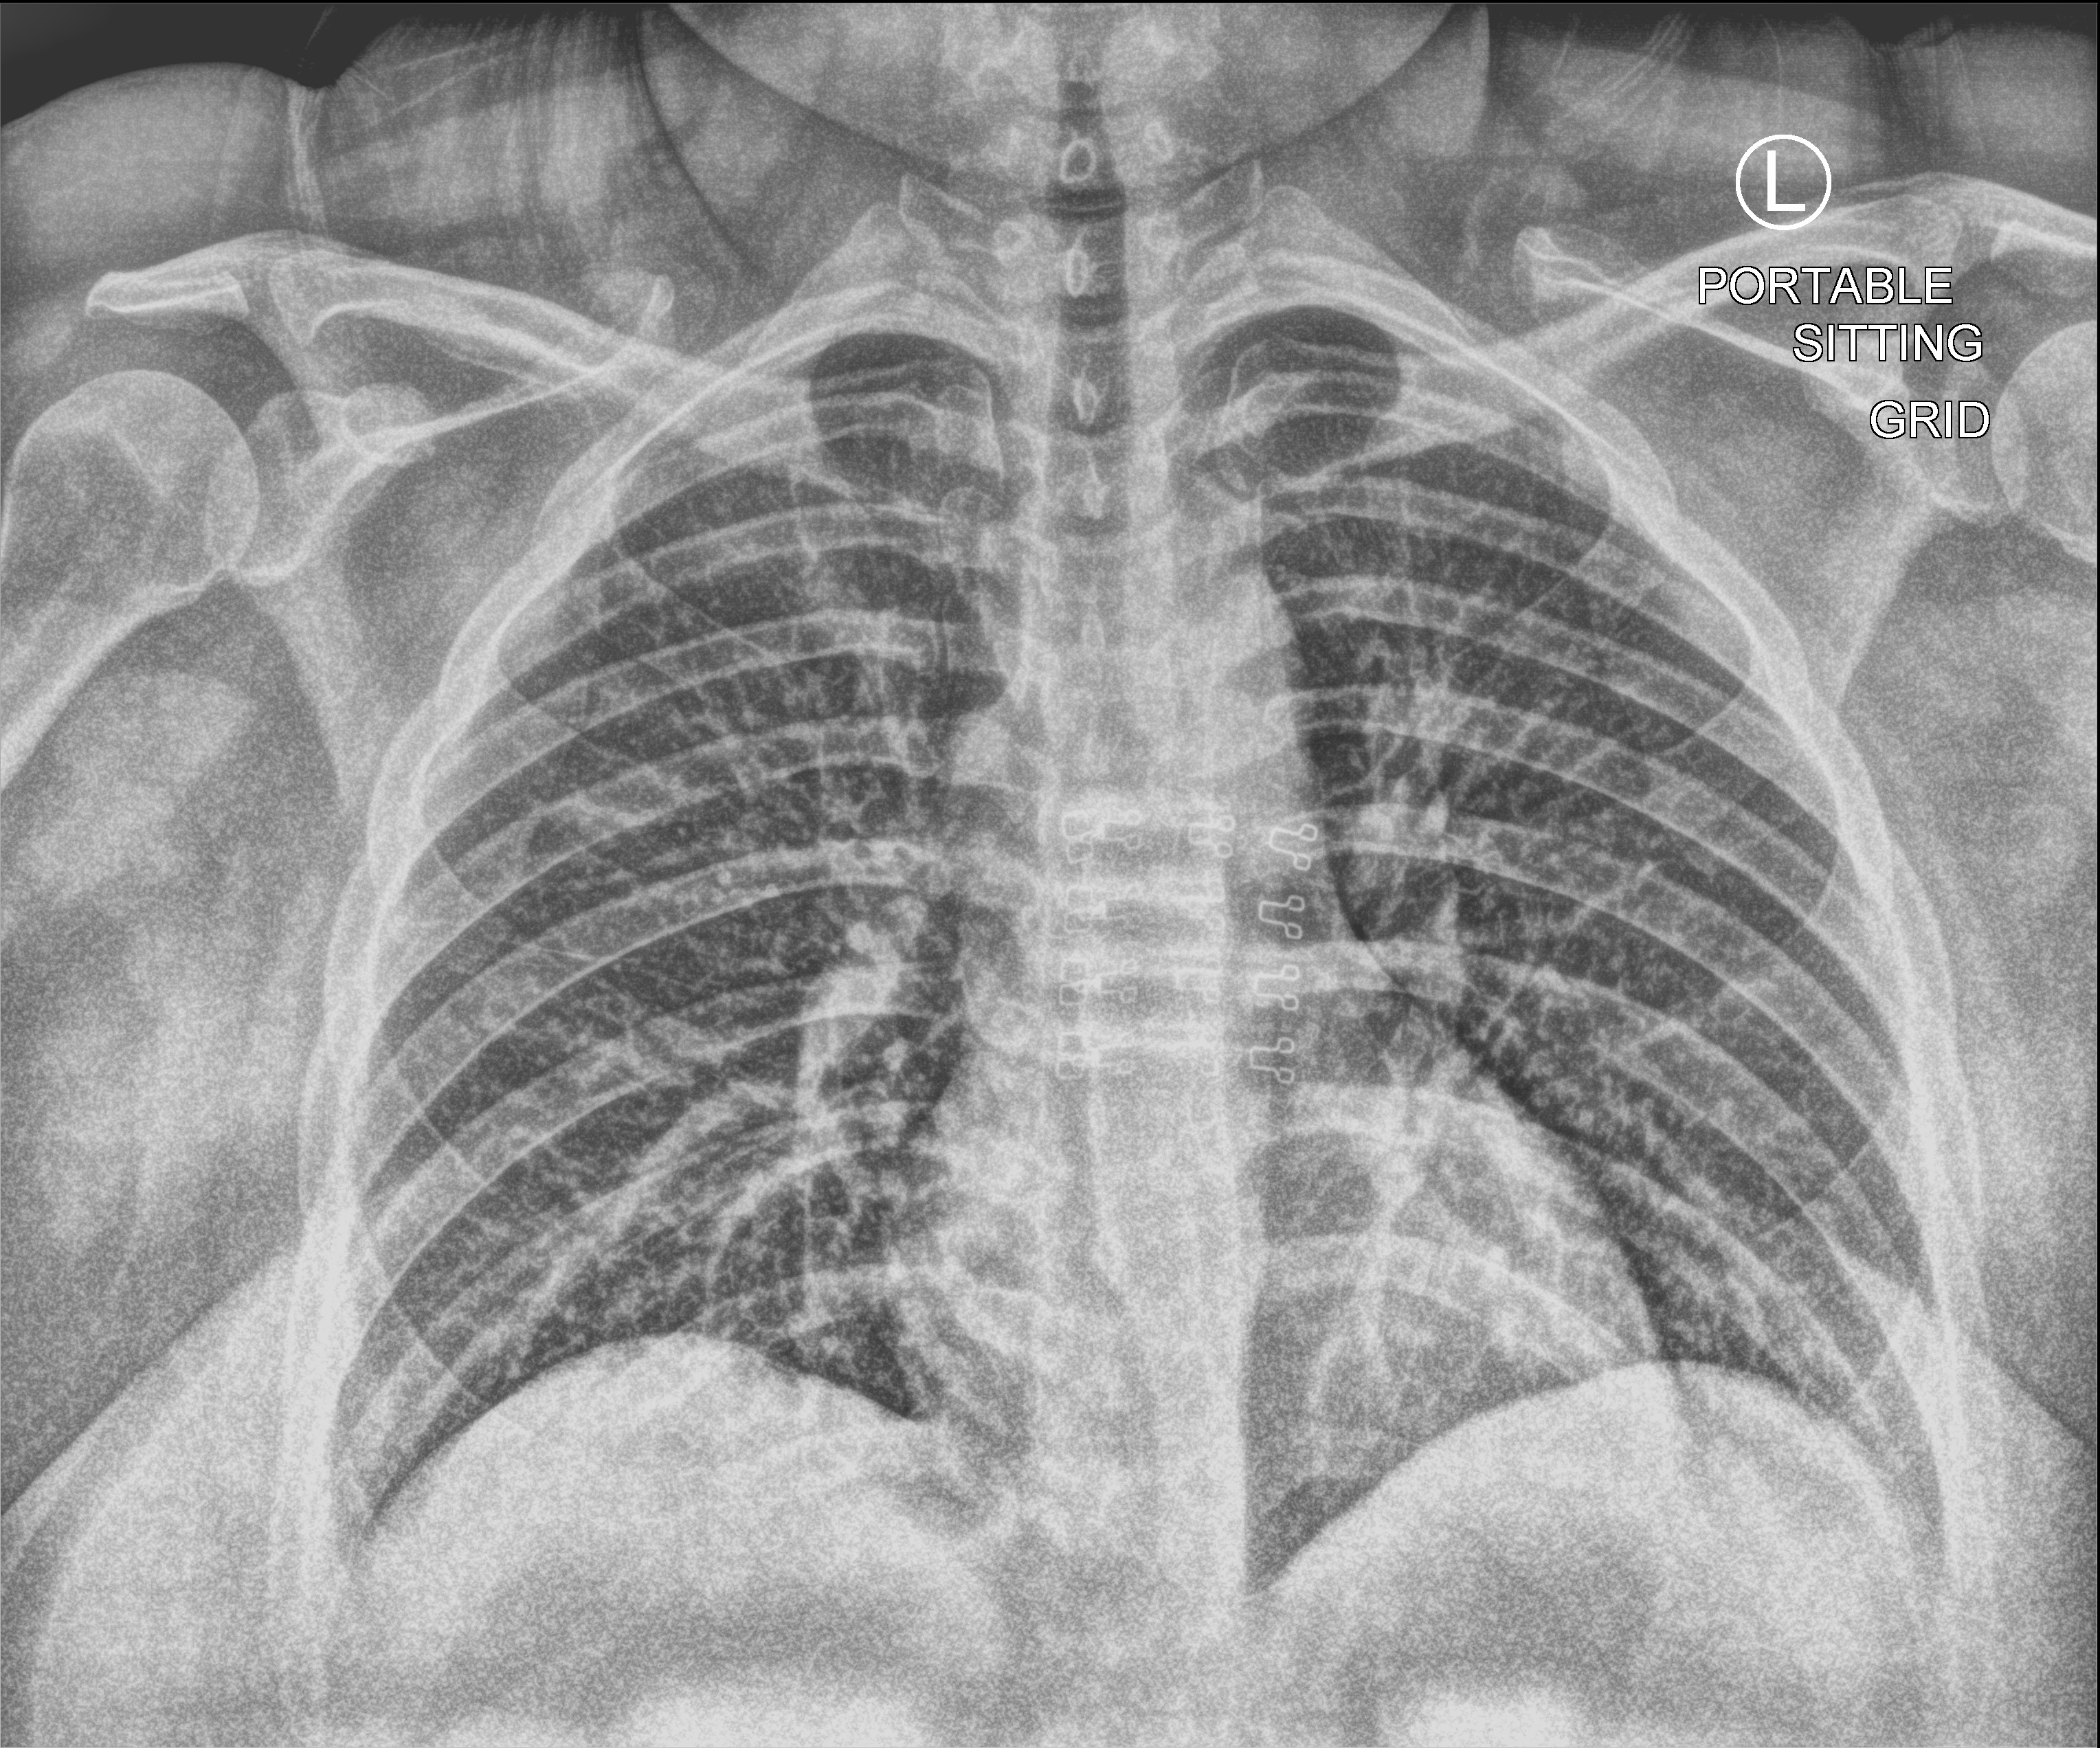
Chest X-ray (portable). Female patient hospitalised with COVID-19, age 18–59 years.
From the hospital-stay record, not from the radiograph (when in the stay this image was taken is not recorded):
- mechanically ventilated during this hospital stay: no
- admitted to intensive care during this hospital stay: no